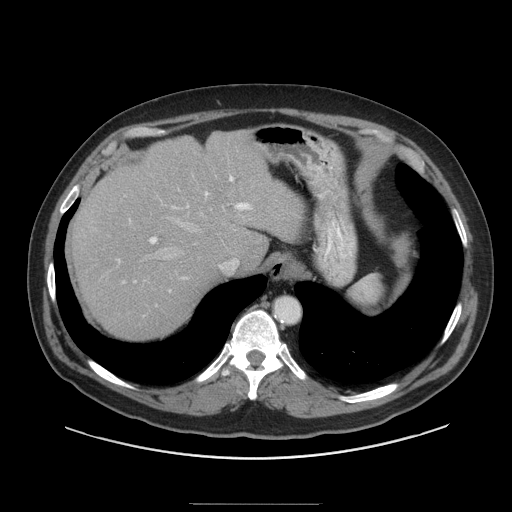
Contrast-enhanced abdominal CT (liver protocol), one axial slice. Slice 73 of 91 in the series (ordered by position). 140 kVp. Soft-tissue window (W 400 / L 40 HU). 512 × 512 image matrix. From the clinical record (not read from this slice): diagnosis: hepatocellular carcinoma (patient treated with transarterial chemoembolisation; whether this scan precedes or follows treatment is not stated here); TNM stage (as recorded): Stage-I; Child-Pugh class: A; tumour differentiation: well differentiated; tumour nodularity: uninodular.
Annotated regions visible in this slice (semi-automatically segmented with operator editing):
- abdominal aorta: bounding box <275,298,299,322> (left, top, right, bottom; pixels)
- liver parenchyma outside the tumour (the mass and vessels are separate outlines, so this box may not span the whole liver): <72,130,304,338>
- mass: <109,268,131,283>
- liver vessels: <118,176,251,282>